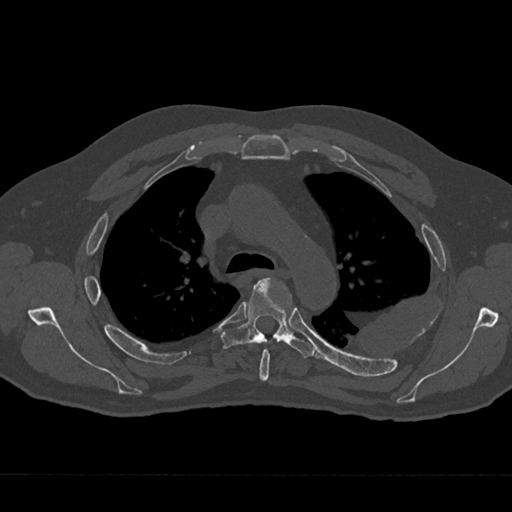
CT including the spine, one axial slice. Position 490 of 797 along the scan axis. Reconstruction kernel Br40s/3. Bone window (W 1800 / L 400 HU). 0.5 mm slice thickness. 512 × 512 image matrix. Male patient, age 75 years. Case-level facts recorded for this patient, not image findings: primary cancer: renal; vertebrae with lytic lesions (as recorded): T4.
Annotated regions visible in this slice (semi-automatically segmented with operator editing):
- T4 vertebra: bounding box [x1, y1, x2, y2] px = [259, 349, 270, 381]
- T5 vertebra: [220, 277, 315, 358]